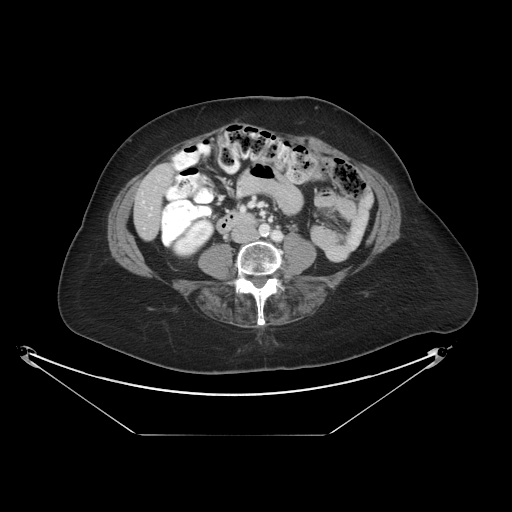
Contrast-enhanced abdominal CT, one axial slice. Position 4 of 36 along the scan axis. 120 kVp. Intravenous contrast given. Soft-tissue window (W 400 / L 40 HU). 512 × 512 image matrix, field of view 500 × 500 mm. Female patient, age 70 years. From the clinical record (not read from this slice): diagnosis: colorectal cancer liver metastases, imaged before liver resection; multiple liver metastases: no; largest metastasis: 2.5 cm; chemotherapy before resection: no.
Outlined on this slice (manually delineated by an expert):
- liver: bounding box (x1, y1, x2, y2) in pixels: (135, 165, 172, 239)